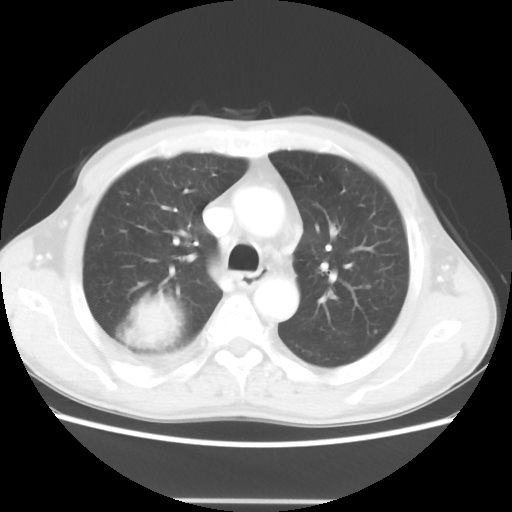
Chest CT, one axial slice; position 35 of 48 along the scan axis; reconstruction kernel STANDARD; 100 kVp; lung window (W 1500 / L -600 HU); 5 mm slice thickness; 512 × 512 image matrix, field of view 361 × 361 mm. Male patient, age 66 years. Case-level facts recorded for this patient, not image findings: clinical TNM (as recorded): T4 N1 M1; histopathological grade: G3.
Structures marked on this image (rectangle marked by the reading radiologist):
- lung tumour (recorded histology: small cell carcinoma): bounding box [x1, y1, x2, y2] px = [127, 288, 185, 351]